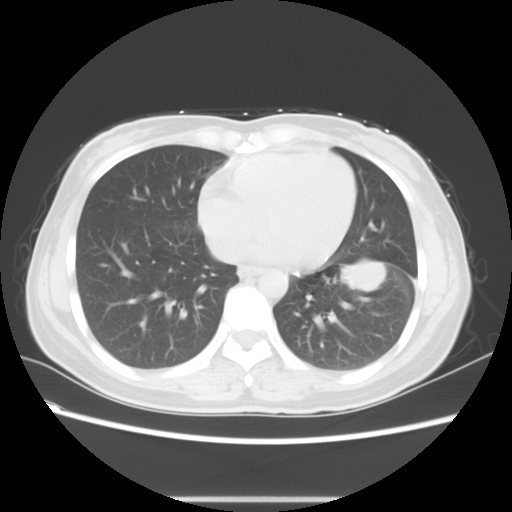
Chest CT, one axial slice. Position 23 of 56 along the scan axis. Reconstruction kernel STANDARD. Lung window (W 1500 / L -600 HU). 5 mm slice thickness. 512 × 512 image matrix, field of view 350 × 350 mm. Patient: female, 41 years. Case-level facts recorded for this patient, not image findings: clinical TNM (as recorded): T1c N3 M1b.
Outlined on this slice (rectangle marked by the reading radiologist):
- lung tumour (recorded histology: adenocarcinoma): box from (x=331, y=248) to (x=395, y=305) px